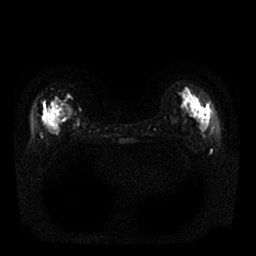
Breast MRI, one axial slice; slice 9 of 25 in the series (ordered by position); diffusion-weighted series; image 2 of 4 stored at this slice position (different b-values; order by instance number); 1.5 T; 256 × 256 image matrix, field of view 340 × 340 mm. Female patient.
Annotated regions visible in this slice (manually delineated by an expert):
- tumour on diffusion-weighted imaging: bounding box [x1, y1, x2, y2] px = [48, 127, 55, 133]